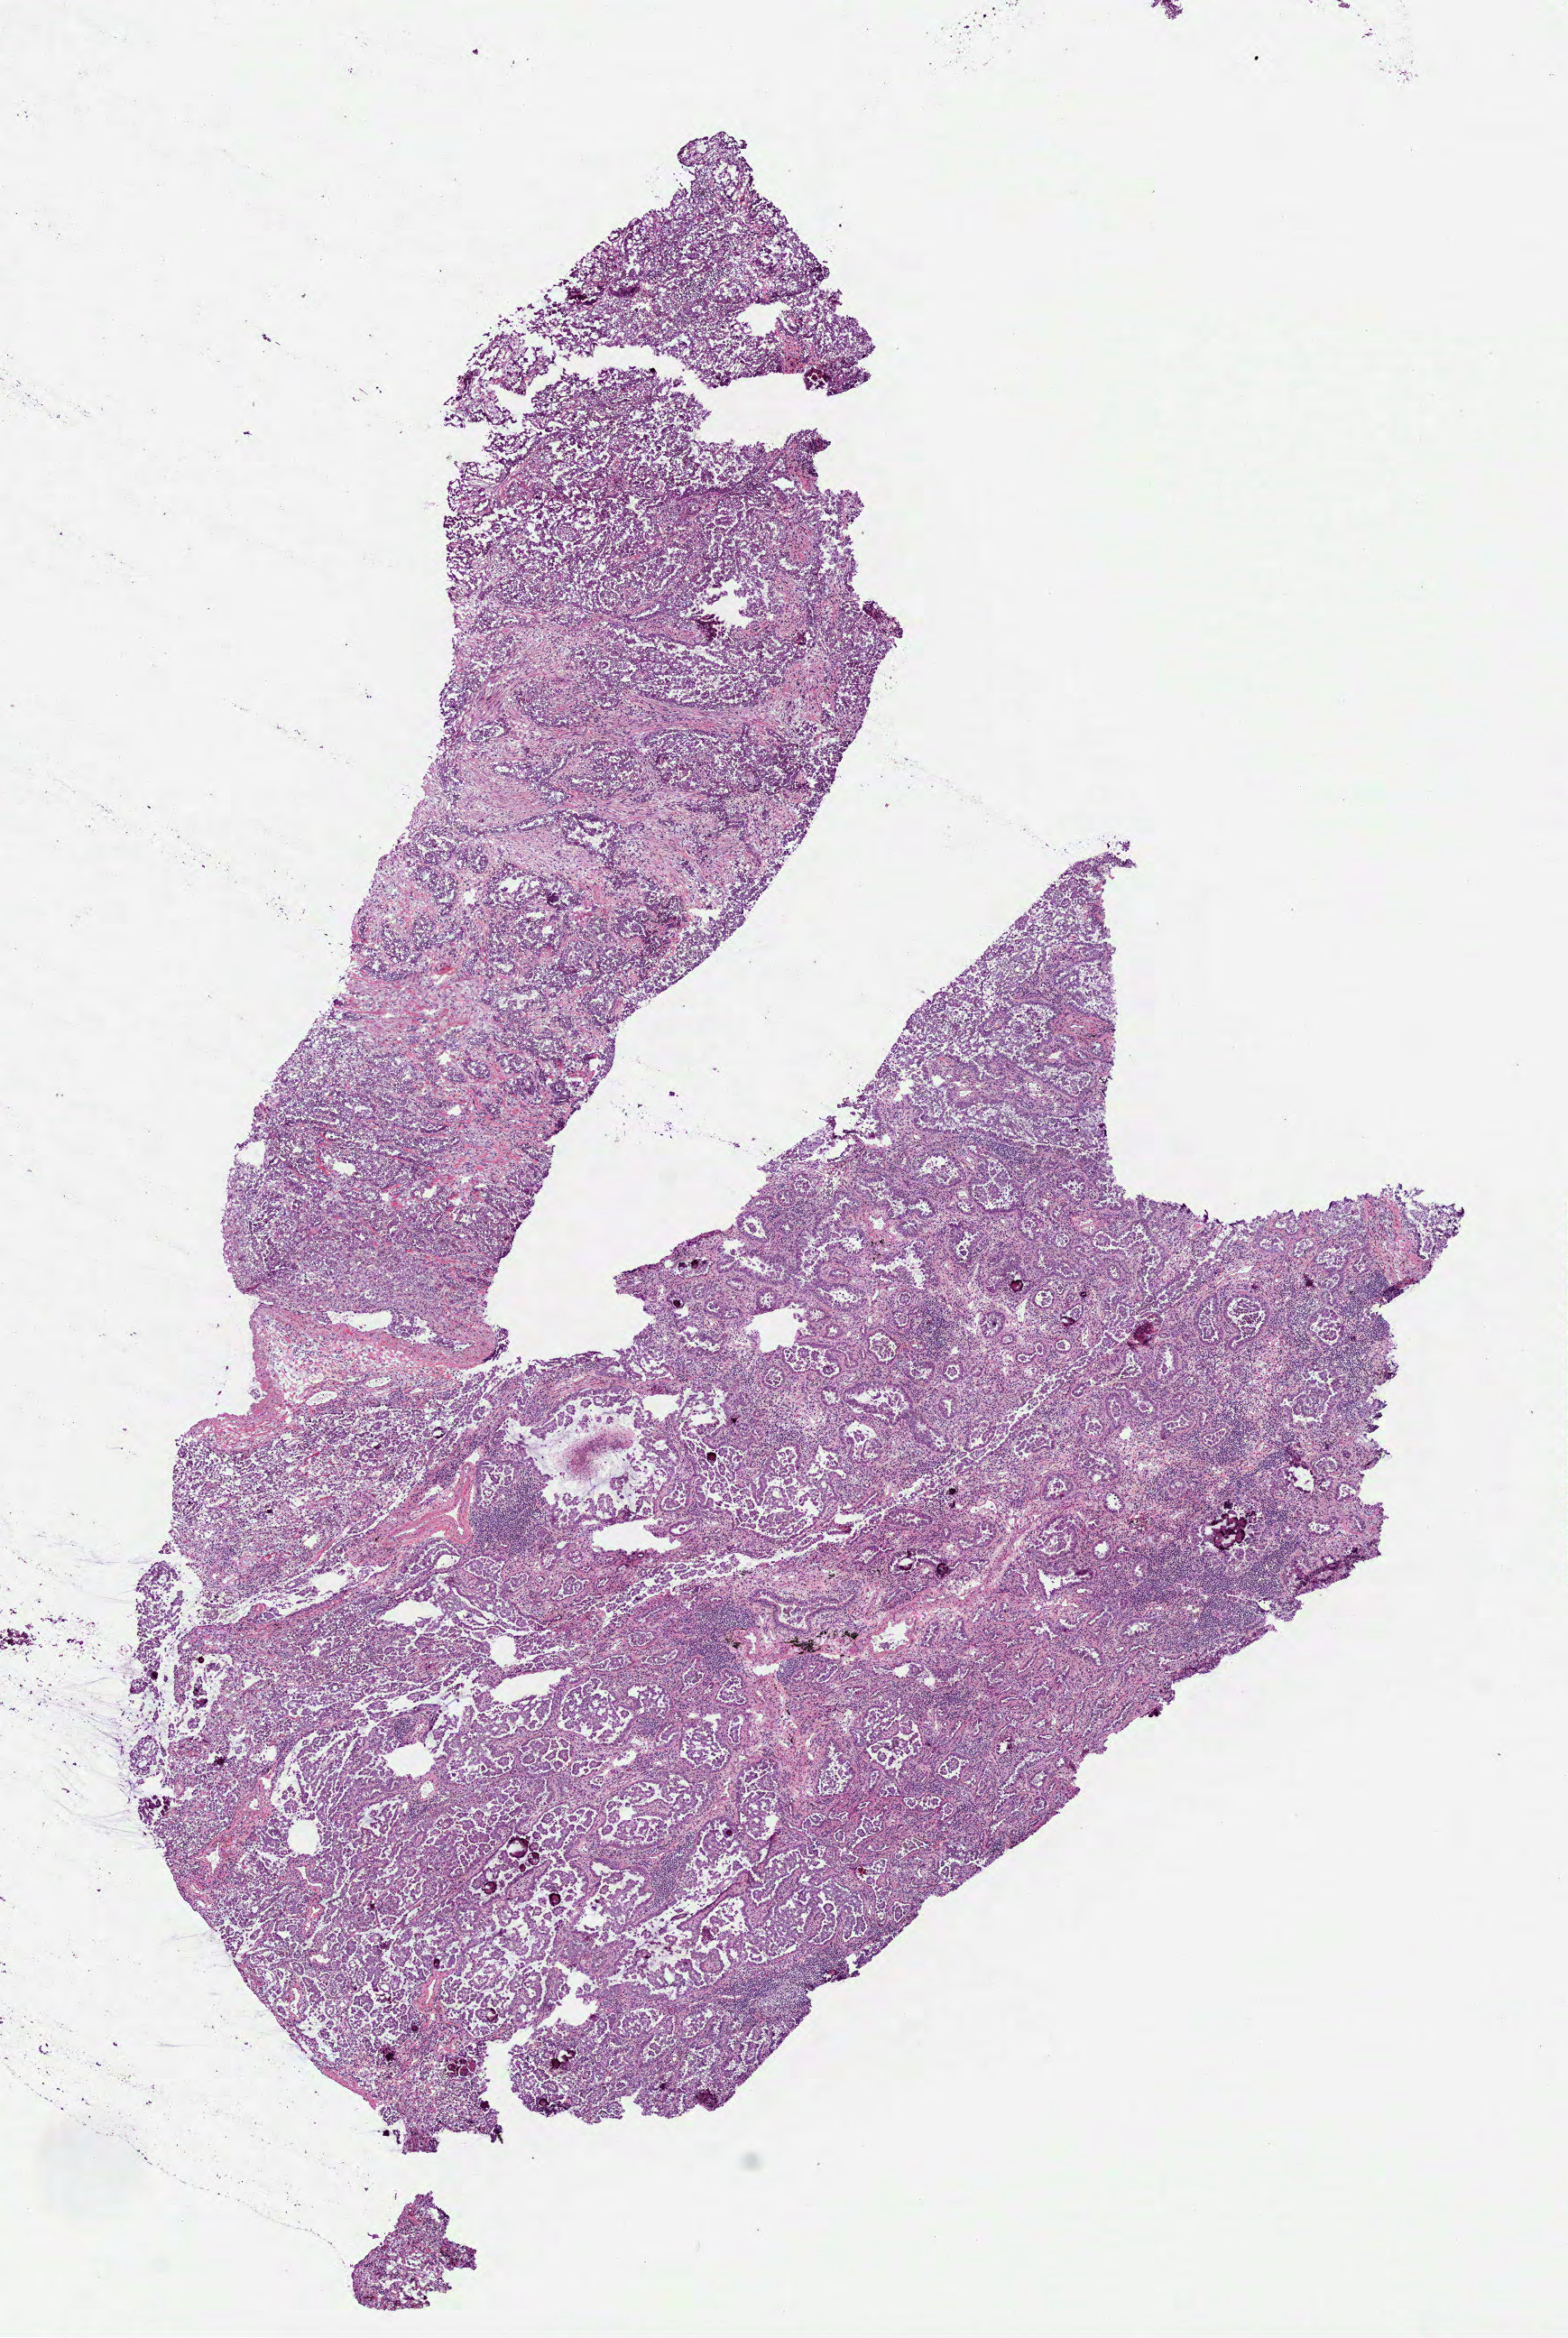
Digitized H&E-stained tissue section (whole slide) — shown as a low-resolution overview of the whole scanned area (about 7.0 x 10.5 mm, from a 40x scan); frozen section from the bottom of the tissue portion; lung, primary tumour sample. Female patient; age at initial diagnosis 57 years. Pathologist review of this section (percent, as recorded): tumour cells 70%, tumour nuclei 40%, normal cells 0%, stromal cells 30%, necrosis 0%.
Pathologic diagnosis: Adenocarcinoma, NOS (middle lobe, lung). AJCC pathologic stage: IA (7th edition).